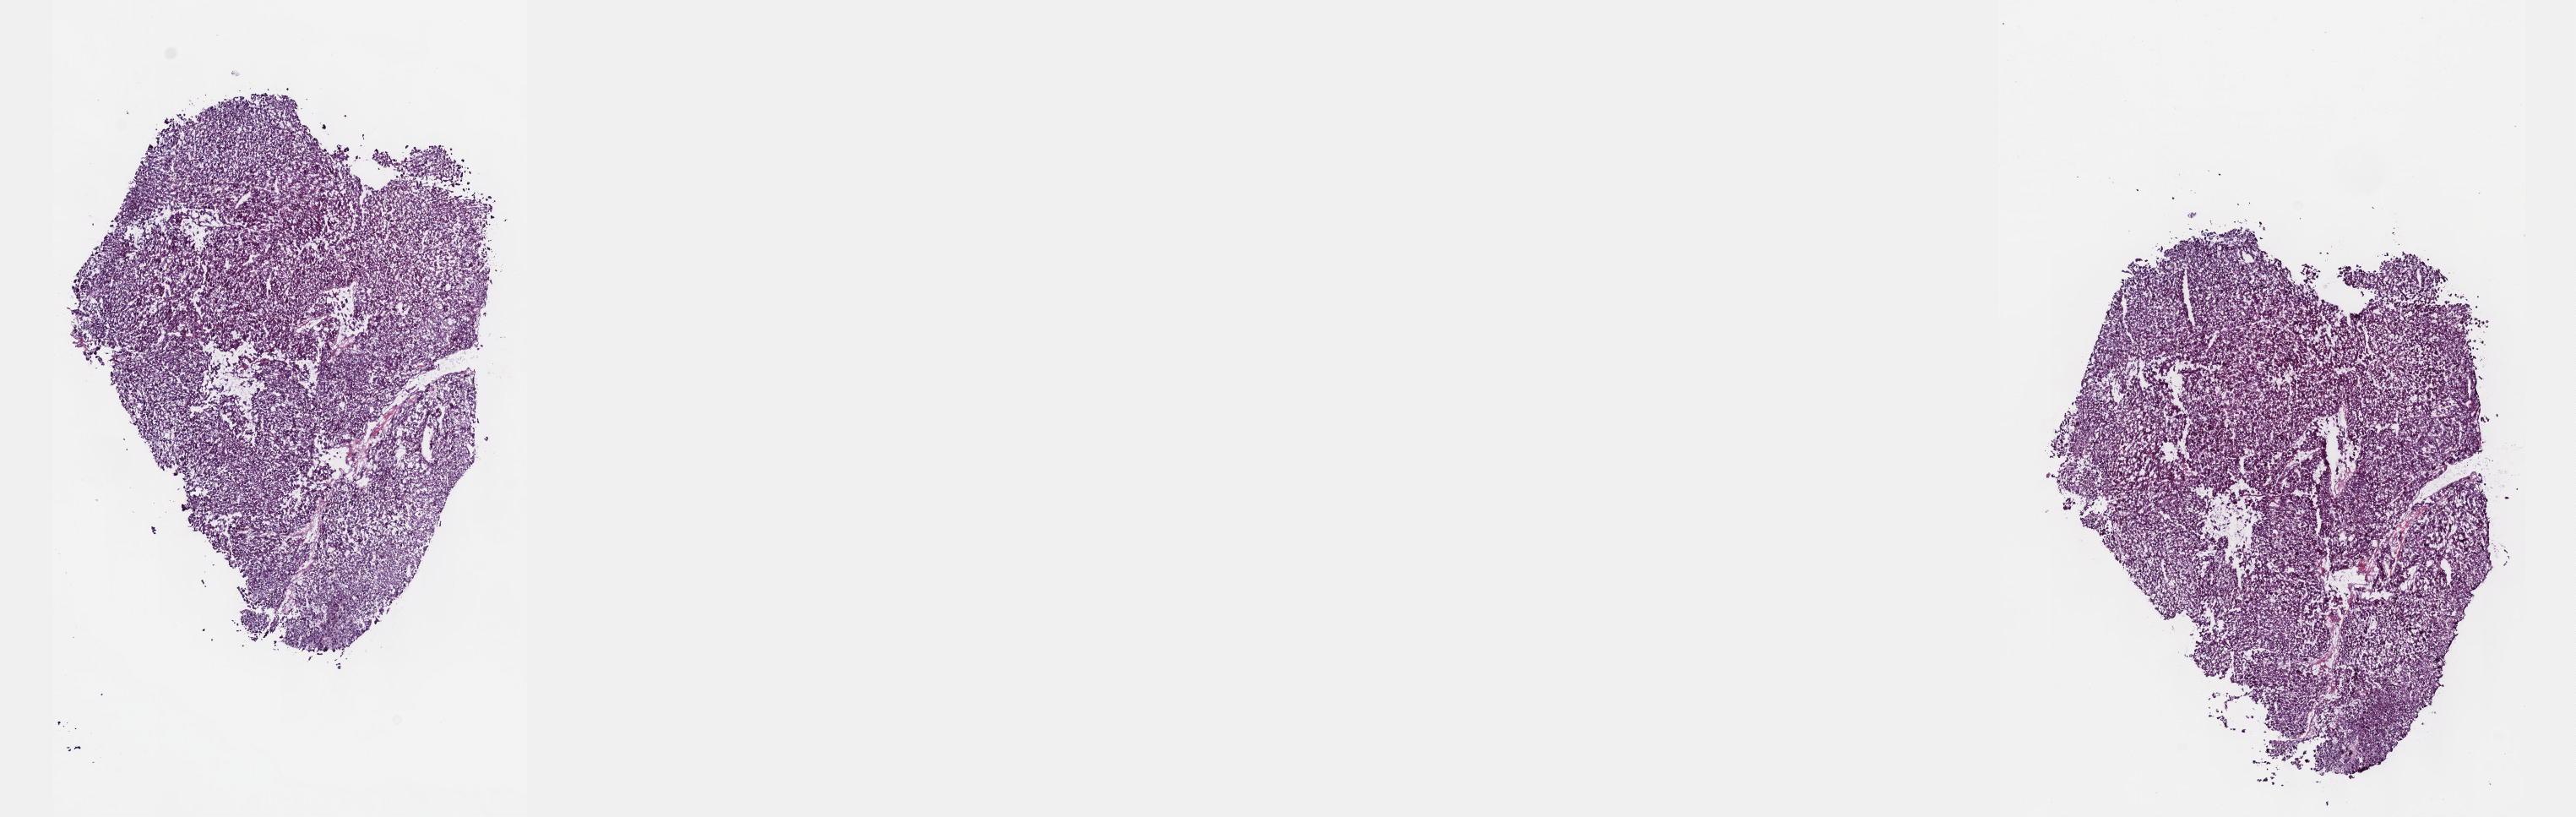
Digitized H&E tissue section (whole slide) — whole scanned area (about 24.6 x 7.8 mm, from a 40x scan) shown as a low-resolution overview, frozen section from the top of the tissue portion, primary tumour sample from the liver. Patient: male, age at initial diagnosis 74 years.
Diagnosis: Hepatocellular carcinoma, NOS.